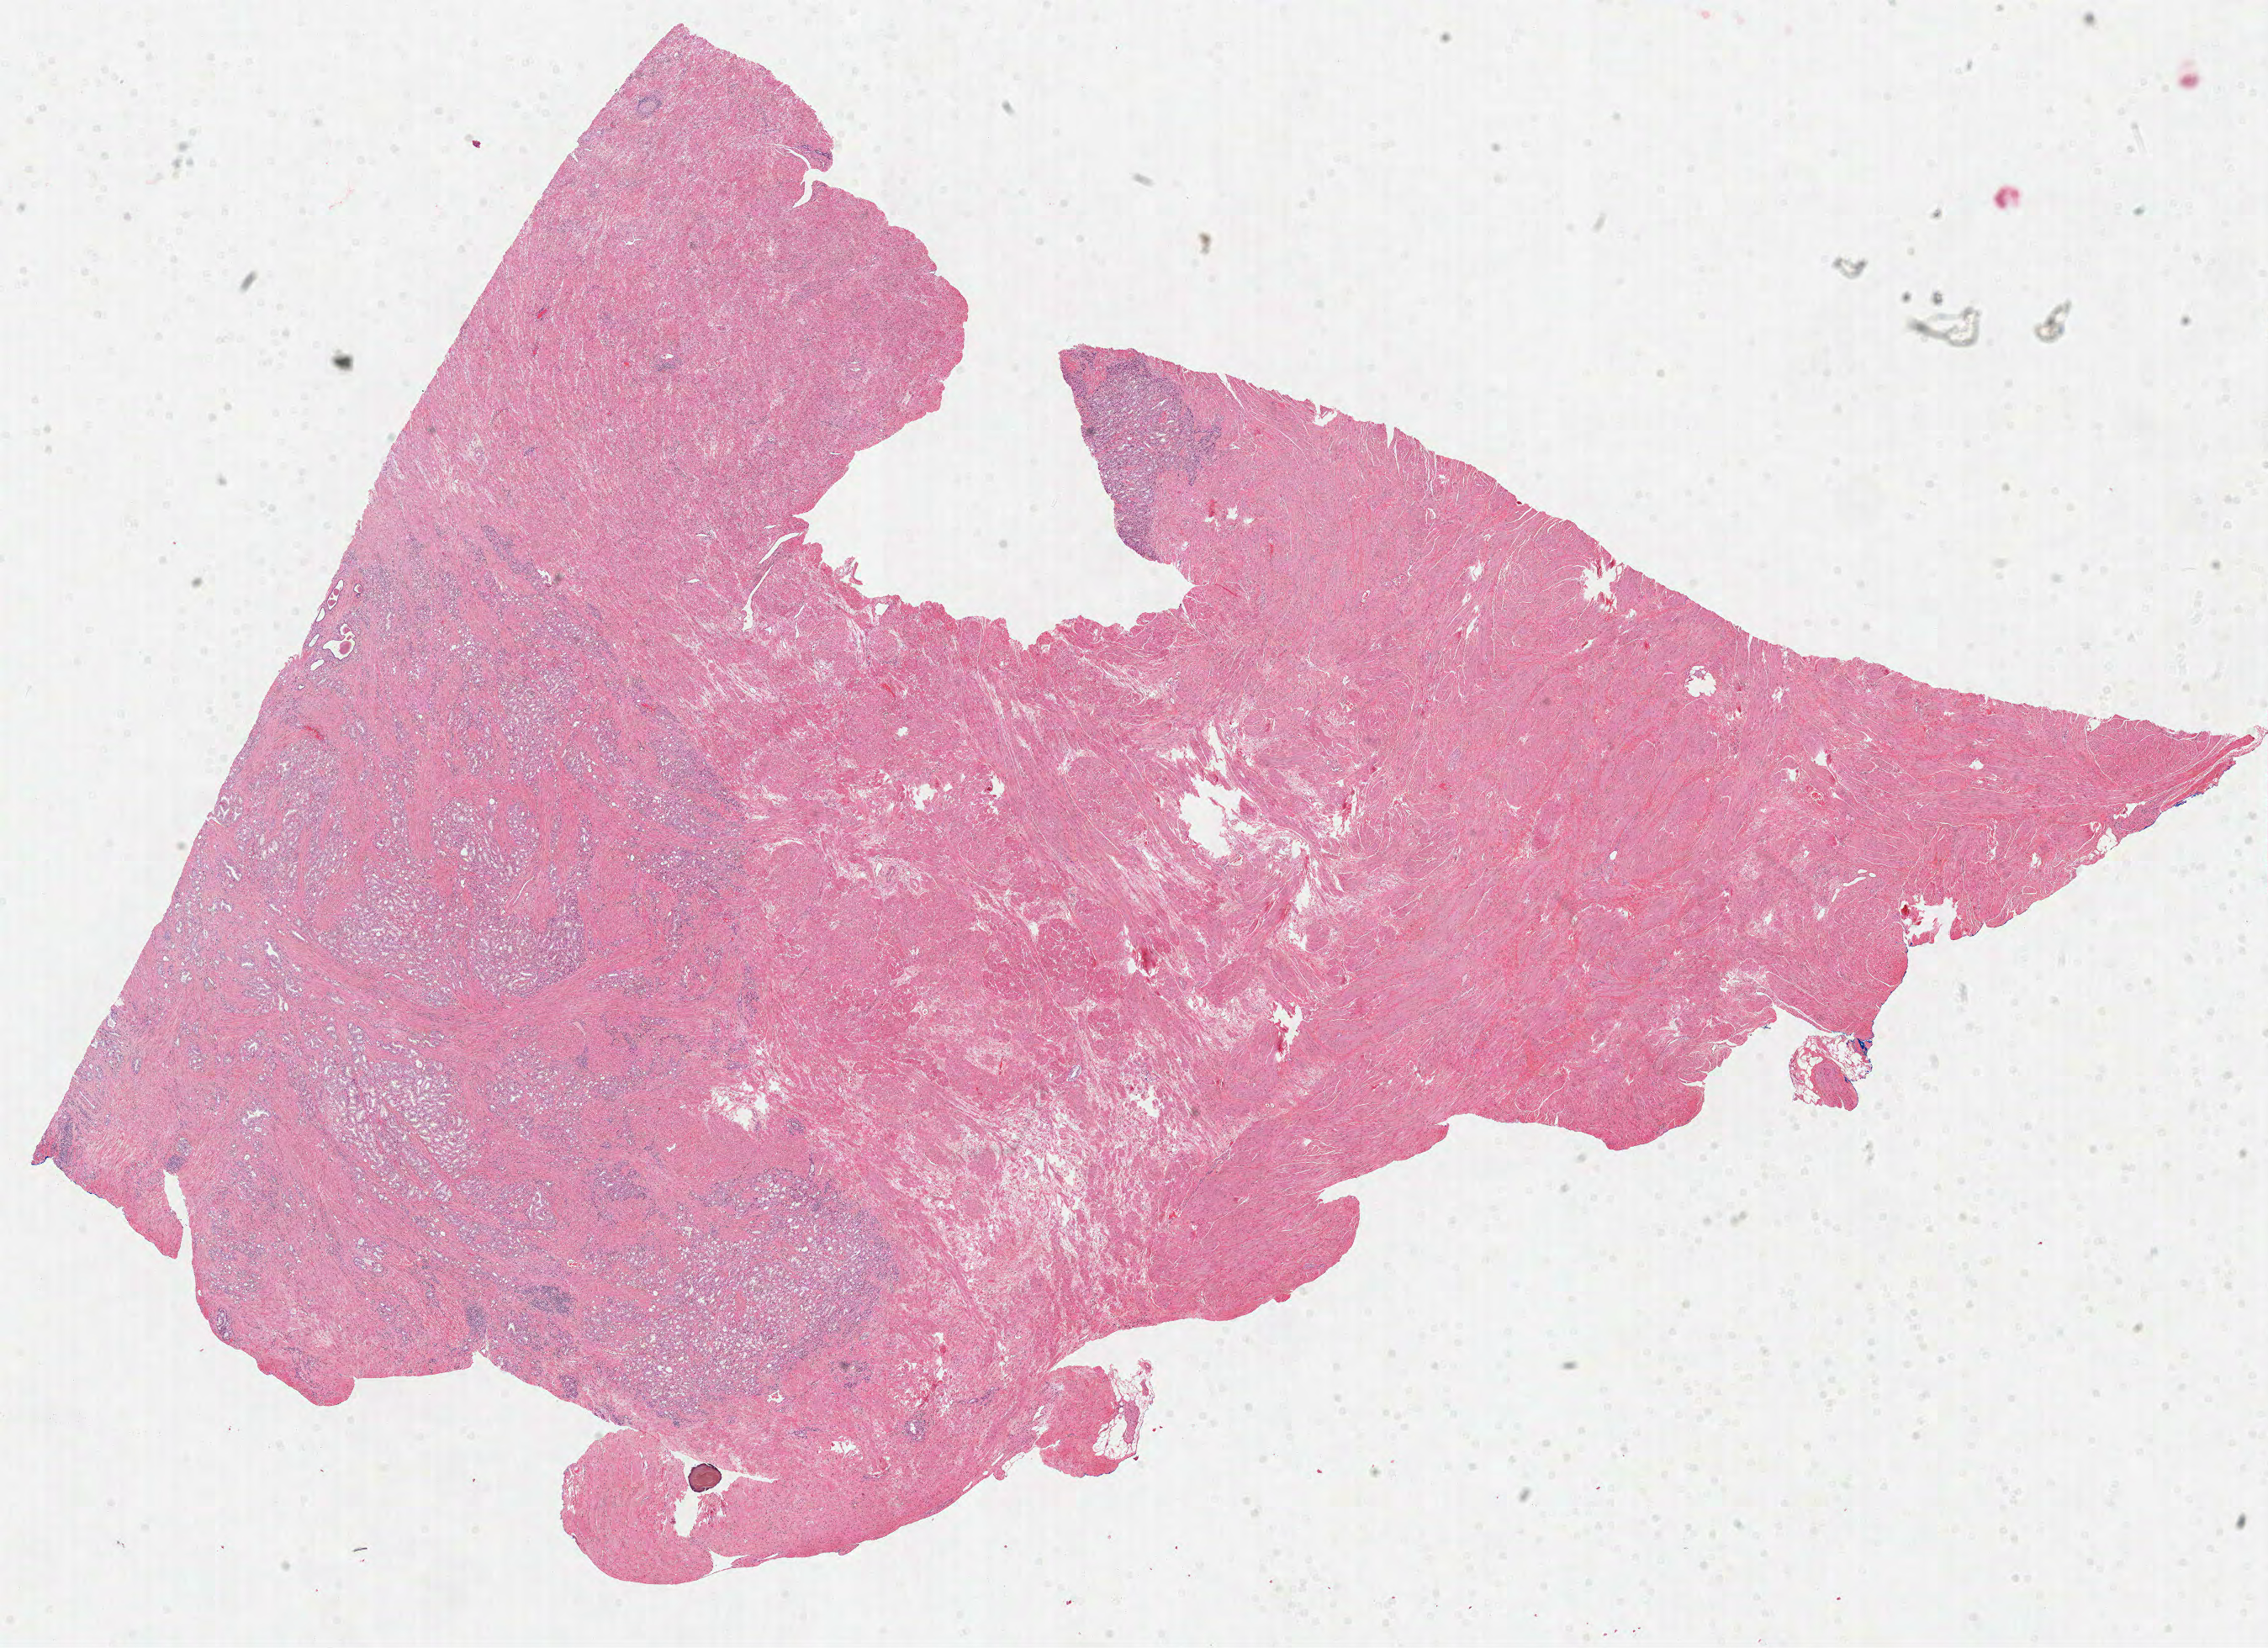
Hematoxylin and eosin (H&E) stained whole-slide image — low-resolution overview of the scanned area, about 21.8 x 15.8 mm (slide scanned at 40x). FFPE section. Primary tumour sample from the prostate. Male, age 66 years at initial diagnosis. Gleason score: 9 (4+5).
Laterality: bilateral. Lymph nodes positive (case pathology): 0 of 3 examined. Histologic diagnosis: Acinar cell carcinoma.